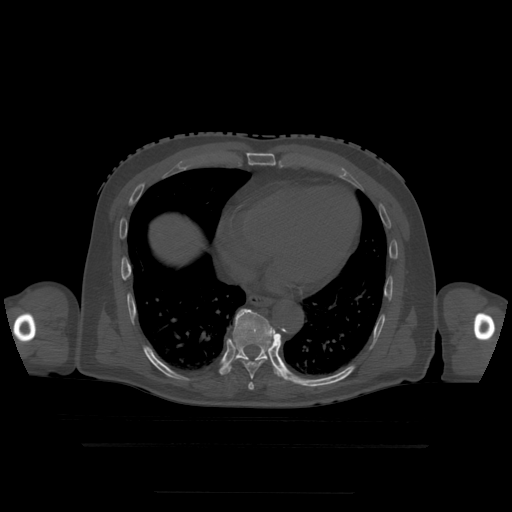
CT including the spine, one axial slice; position 271 of 522 along the scan axis; bone window (W 1800 / L 400 HU); 512 × 512 image matrix, field of view 436 × 436 mm. Patient age 68 years. From the clinical record (not read from this slice): primary cancer: urothelial.
Outlined on this slice (semi-automatic segmentation, software-assisted and operator-edited):
- T7 vertebra: box from (x=248, y=383) to (x=254, y=390) px
- T8 vertebra: (x=244, y=357)–(x=272, y=379)
- T9 vertebra: (x=222, y=309)–(x=284, y=378)